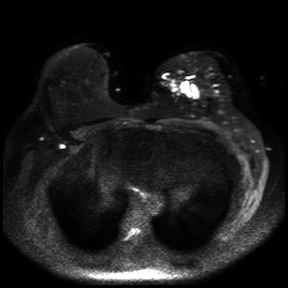
Breast MRI, one axial slice; diffusion-weighted series; image 2 of 4 stored at this slice position (different b-values; order by instance number); 3 T; 4 mm slice thickness; 288 × 288 image matrix, field of view 360 × 360 mm. Female patient.
Outlined on this slice (outlined manually by an expert reader):
- tumour on diffusion-weighted imaging: bounding box <179,81,198,97> (left, top, right, bottom; pixels)